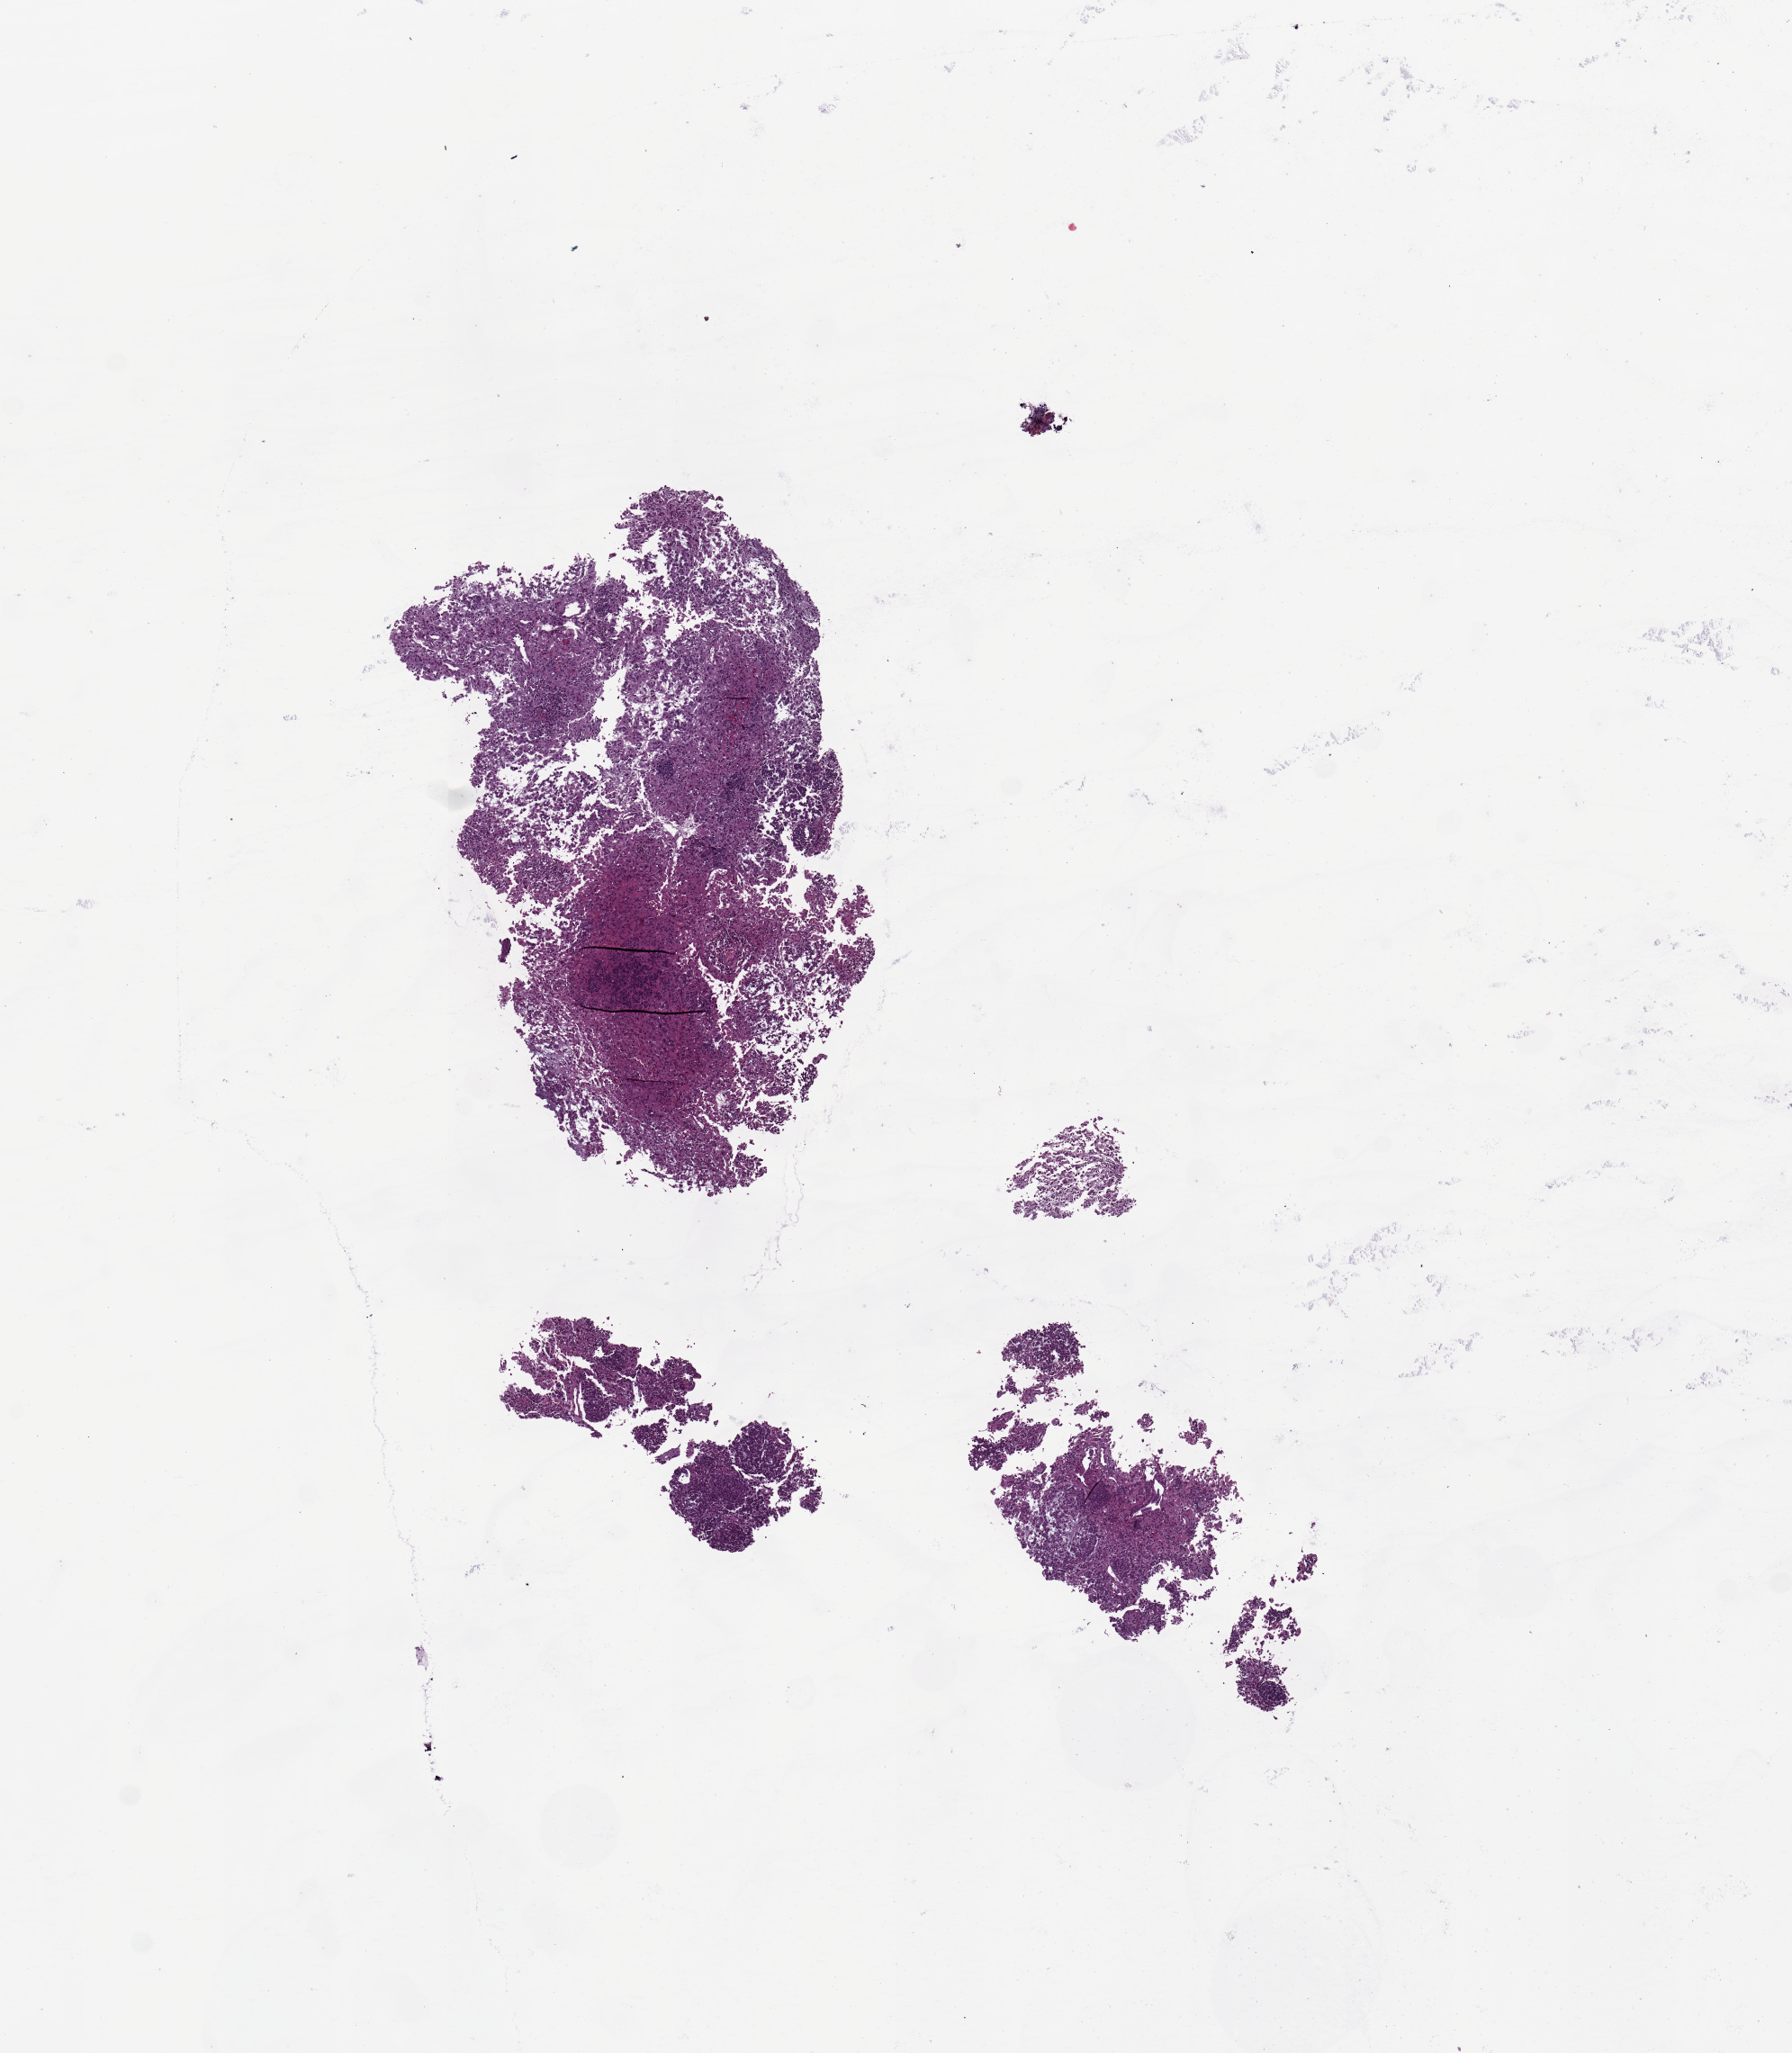
Hematoxylin and eosin (H&E) stained whole-slide image, low-resolution overview of the scanned area, about 7.9 x 9.0 mm; tumour tissue sample, brain. Patient: male, age 53 years.
- diagnosis: Glioblastoma